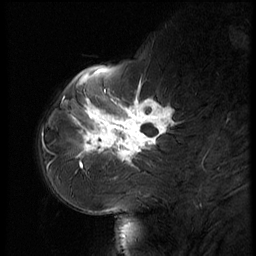
Breast MRI (dynamic contrast-enhanced), one sagittal slice; position 19 of 56 along the scan axis; dynamic contrast-enhanced series, image 2 of 3 at this slice position (ordered by acquisition); 1.5 T; TE 4.2 ms, TR 9 ms; 256 × 256 image matrix. Female patient, age 61 years. Case-level facts recorded for this patient, not image findings: setting: breast cancer imaged before/during neoadjuvant chemotherapy; receptor status: HR-positive, HER2-negative.
Outlined on this slice (semi-automatically segmented with operator editing):
- analysis volume of interest (the breast-tissue region the enhancement analysis was run in; not a lesion): bounding box [x1, y1, x2, y2] px = [65, 74, 185, 175]
- tumour enhancement mask (voxels above the 140 % enhancement threshold inside the analysis volume of interest): [76, 91, 173, 168]